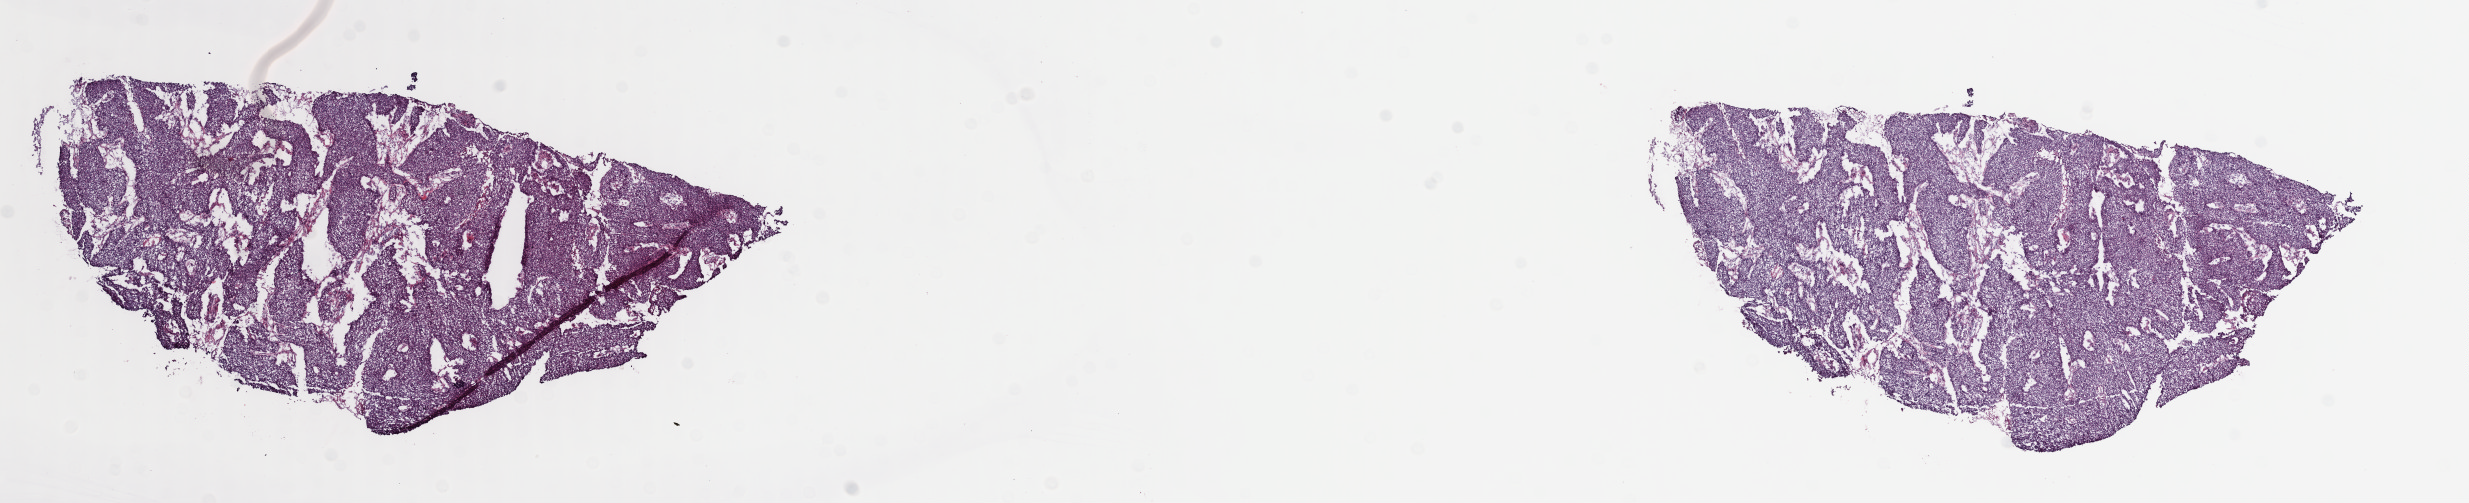
Hematoxylin and eosin (H&E) stained whole-slide image, shown as a low-resolution overview of the whole scanned area (about 19.5 x 4.0 mm, acquisition: 40x scan); frozen section from the top of the tissue portion; cervix, primary tumour sample. Patient: female, age at initial diagnosis 37 years. Histologic grade: G1 (well differentiated). Slide review estimates, as recorded: tumour cells 90%, tumour nuclei 90%, normal cells 0%, stromal cells 5%, necrosis 5%. Inflammatory infiltration, as recorded: lymphocyte infiltration 40%, monocyte infiltration 20%, neutrophil infiltration 20%.
• FIGO stage: IB2
• histologic diagnosis: Squamous cell carcinoma, NOS (cervix uteri)